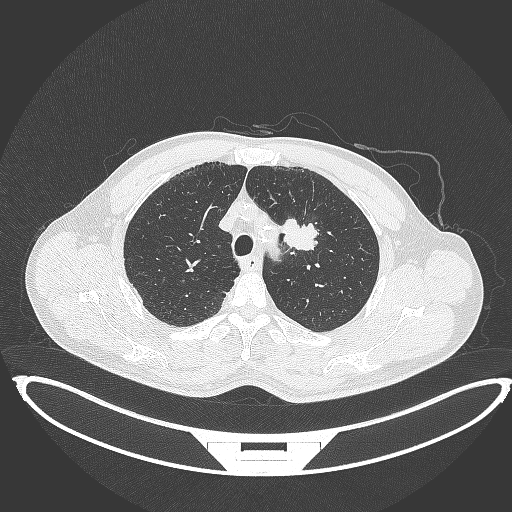
Chest CT, one axial slice. Reconstruction kernel B70f. 120 kVp. Lung window (W 1500 / L -600 HU). 512 × 512 image matrix, field of view 457 × 457 mm. Male patient, age 60 years. From the clinical record (not read from this slice): clinical TNM (as recorded): T2a N0 M0; histopathological grade: G1-G2.
Structures marked on this image (bounding box drawn by a radiologist):
- lung tumour (recorded histology: squamous cell carcinoma): bounding box <279,215,320,252> (left, top, right, bottom; pixels)